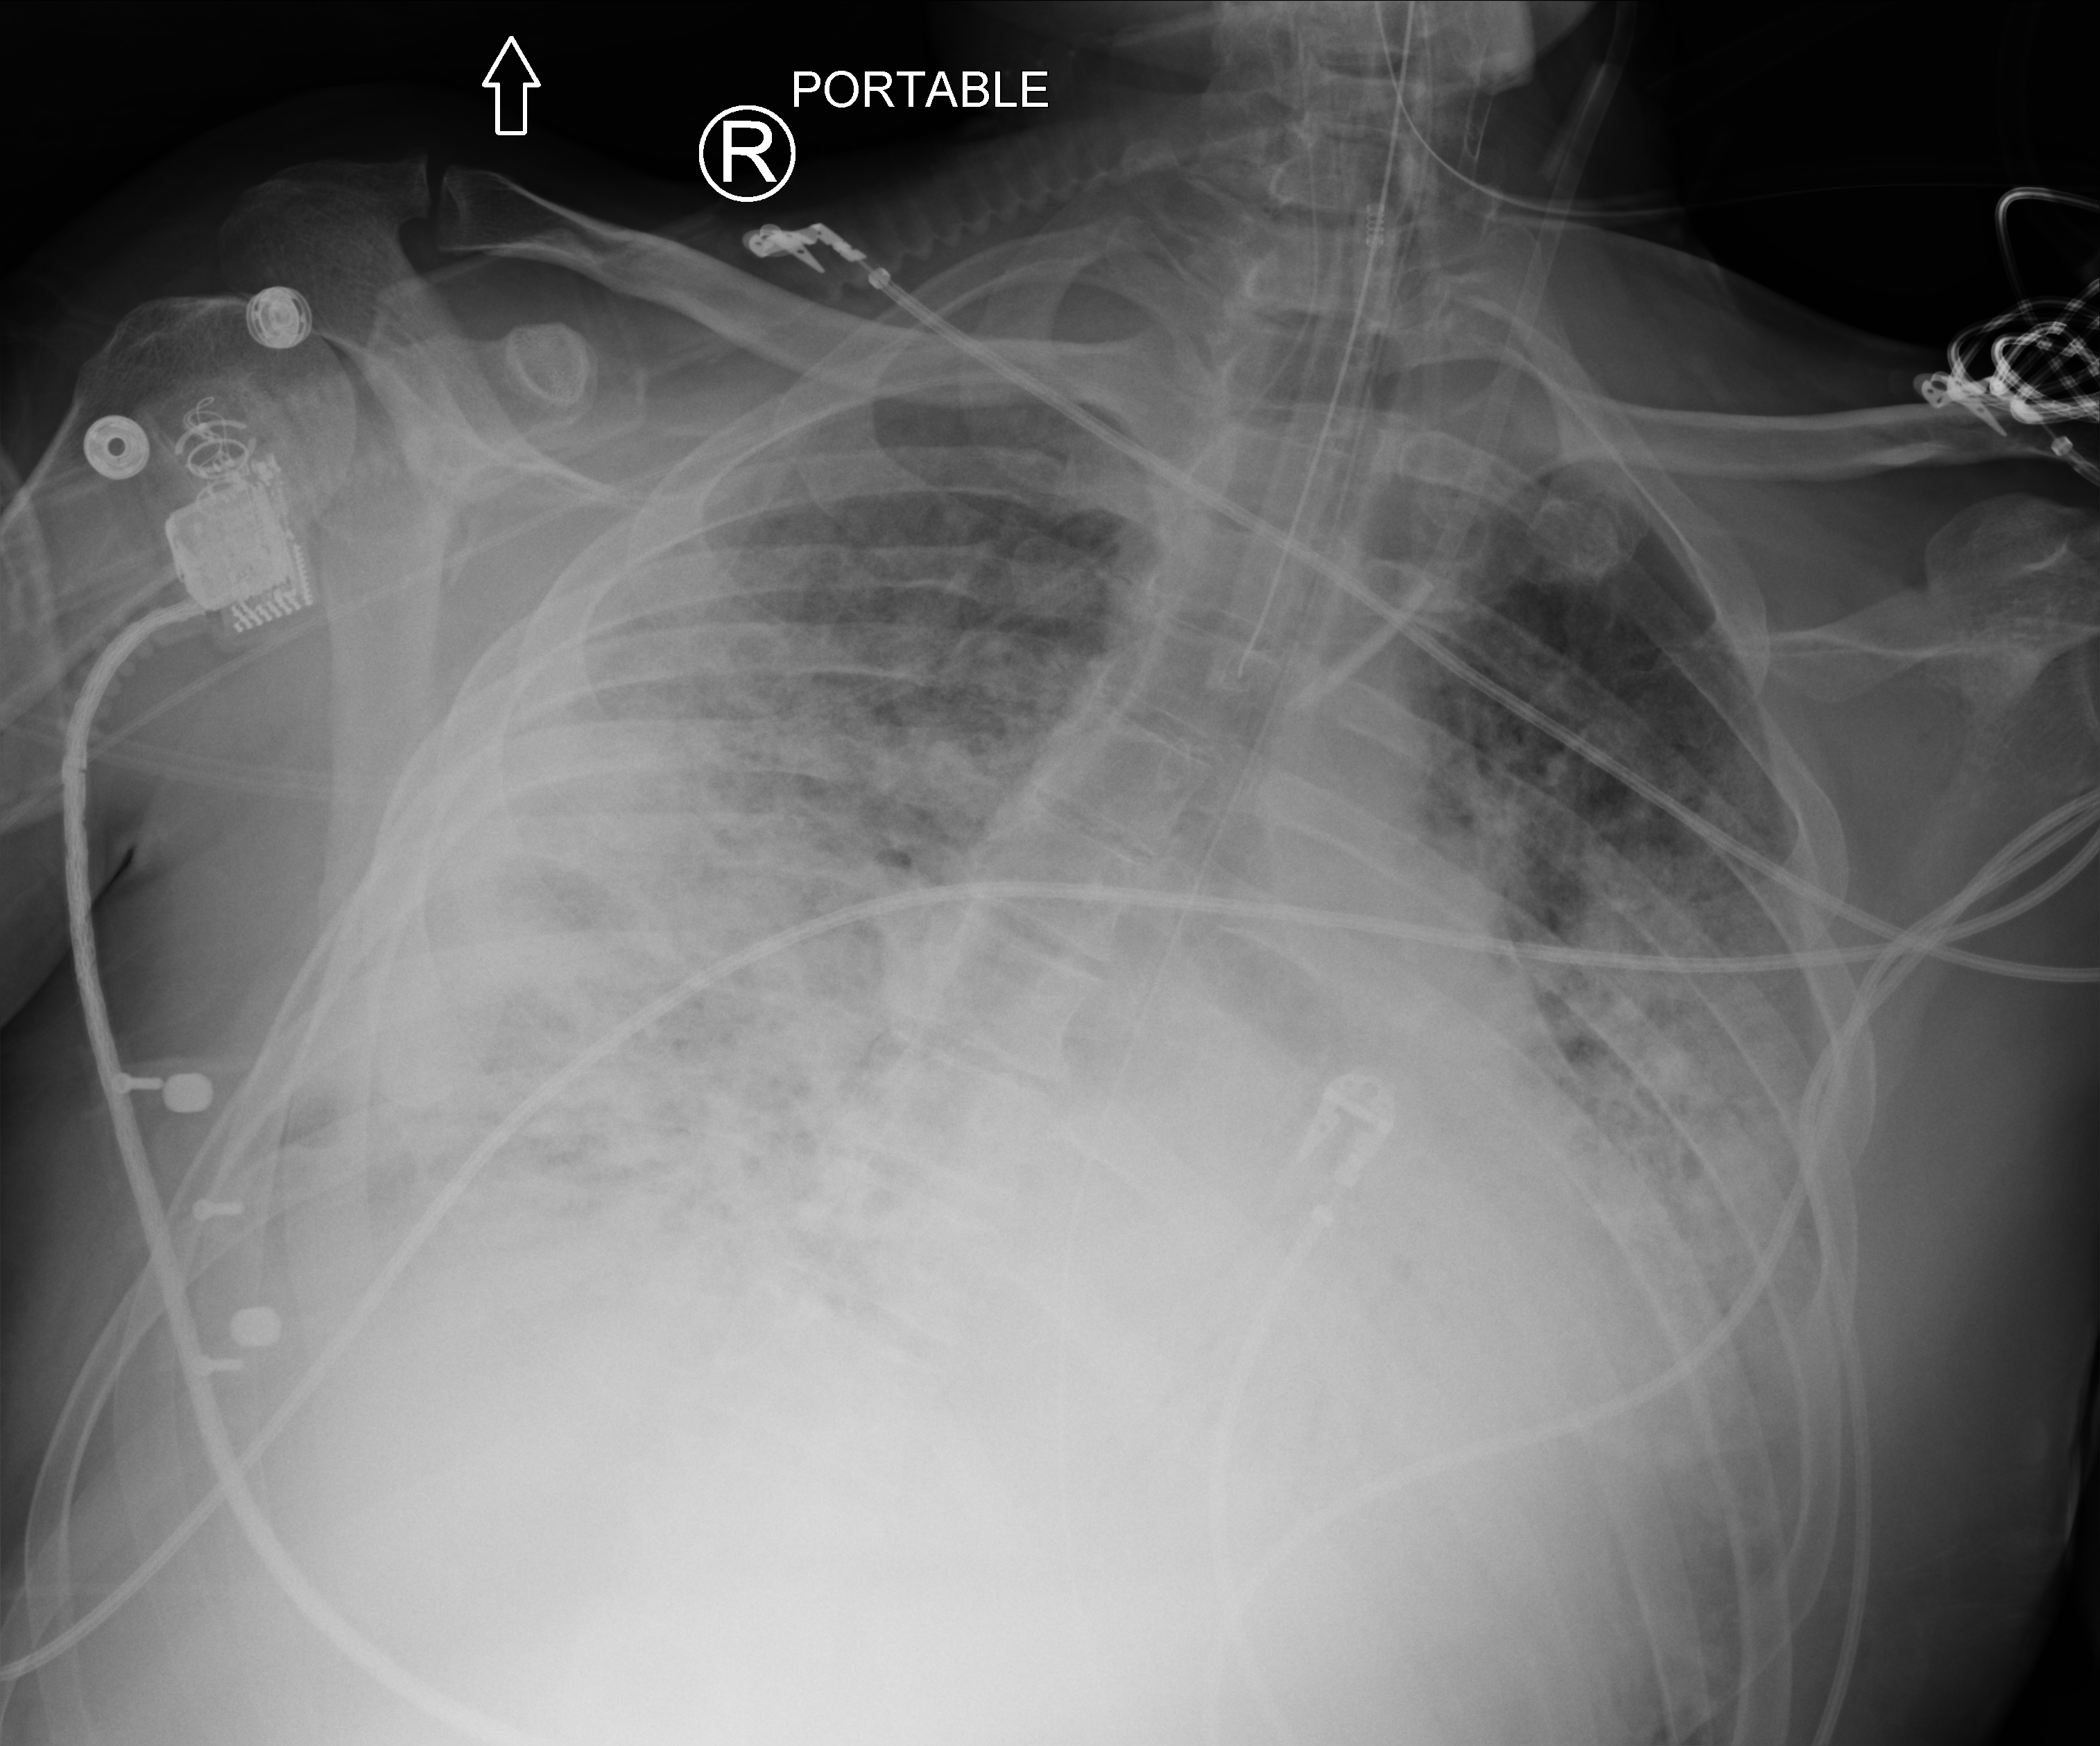
Chest X-ray (portable); anteroposterior (AP) projection. Patient hospitalised with COVID-19; male, aged 18–59 years.
Hospital-stay facts (about this admission, not read from this image; timing relative to this image not recorded):
- admitted to intensive care during this hospital stay: yes
- COPD (admission record): no
- length of hospital stay: 75 days